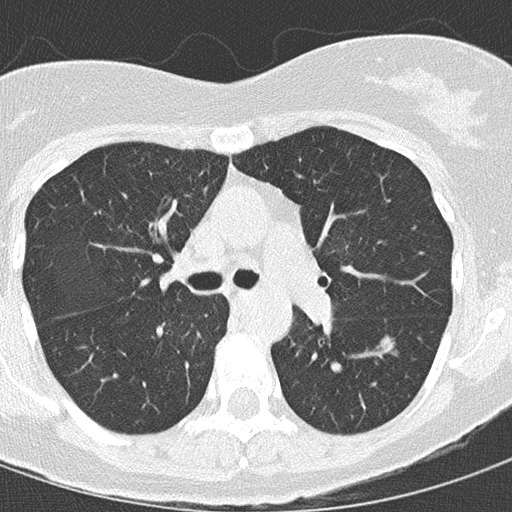
Axial slice from a low-dose chest CT screening exam. Baseline screening round. Lung window (W 1500 / L -600 HU). 2 mm slice thickness. Slice 54 of 145 in the series. 512 × 512 image matrix. Female, age 68 years at enrolment. Current smoker at enrolment.
- Lesion marked by an expert reader, bounding box [x1, y1, x2, y2] px = [370, 324, 415, 366].
- The exam's reader record, not a measurement of the box and not confirmed to be the same lesion: non-calcified nodule or mass ≥4 mm, left lower lobe, 15 × 15 mm, mixed attenuation.
- Participant outcome: lung cancer diagnosed 72 days after this screen — bronchiolo-alveolar adenocarcinoma, NOS, left lower lobe, stage IIIB (AJCC 6th edition), 12 mm at pathology.